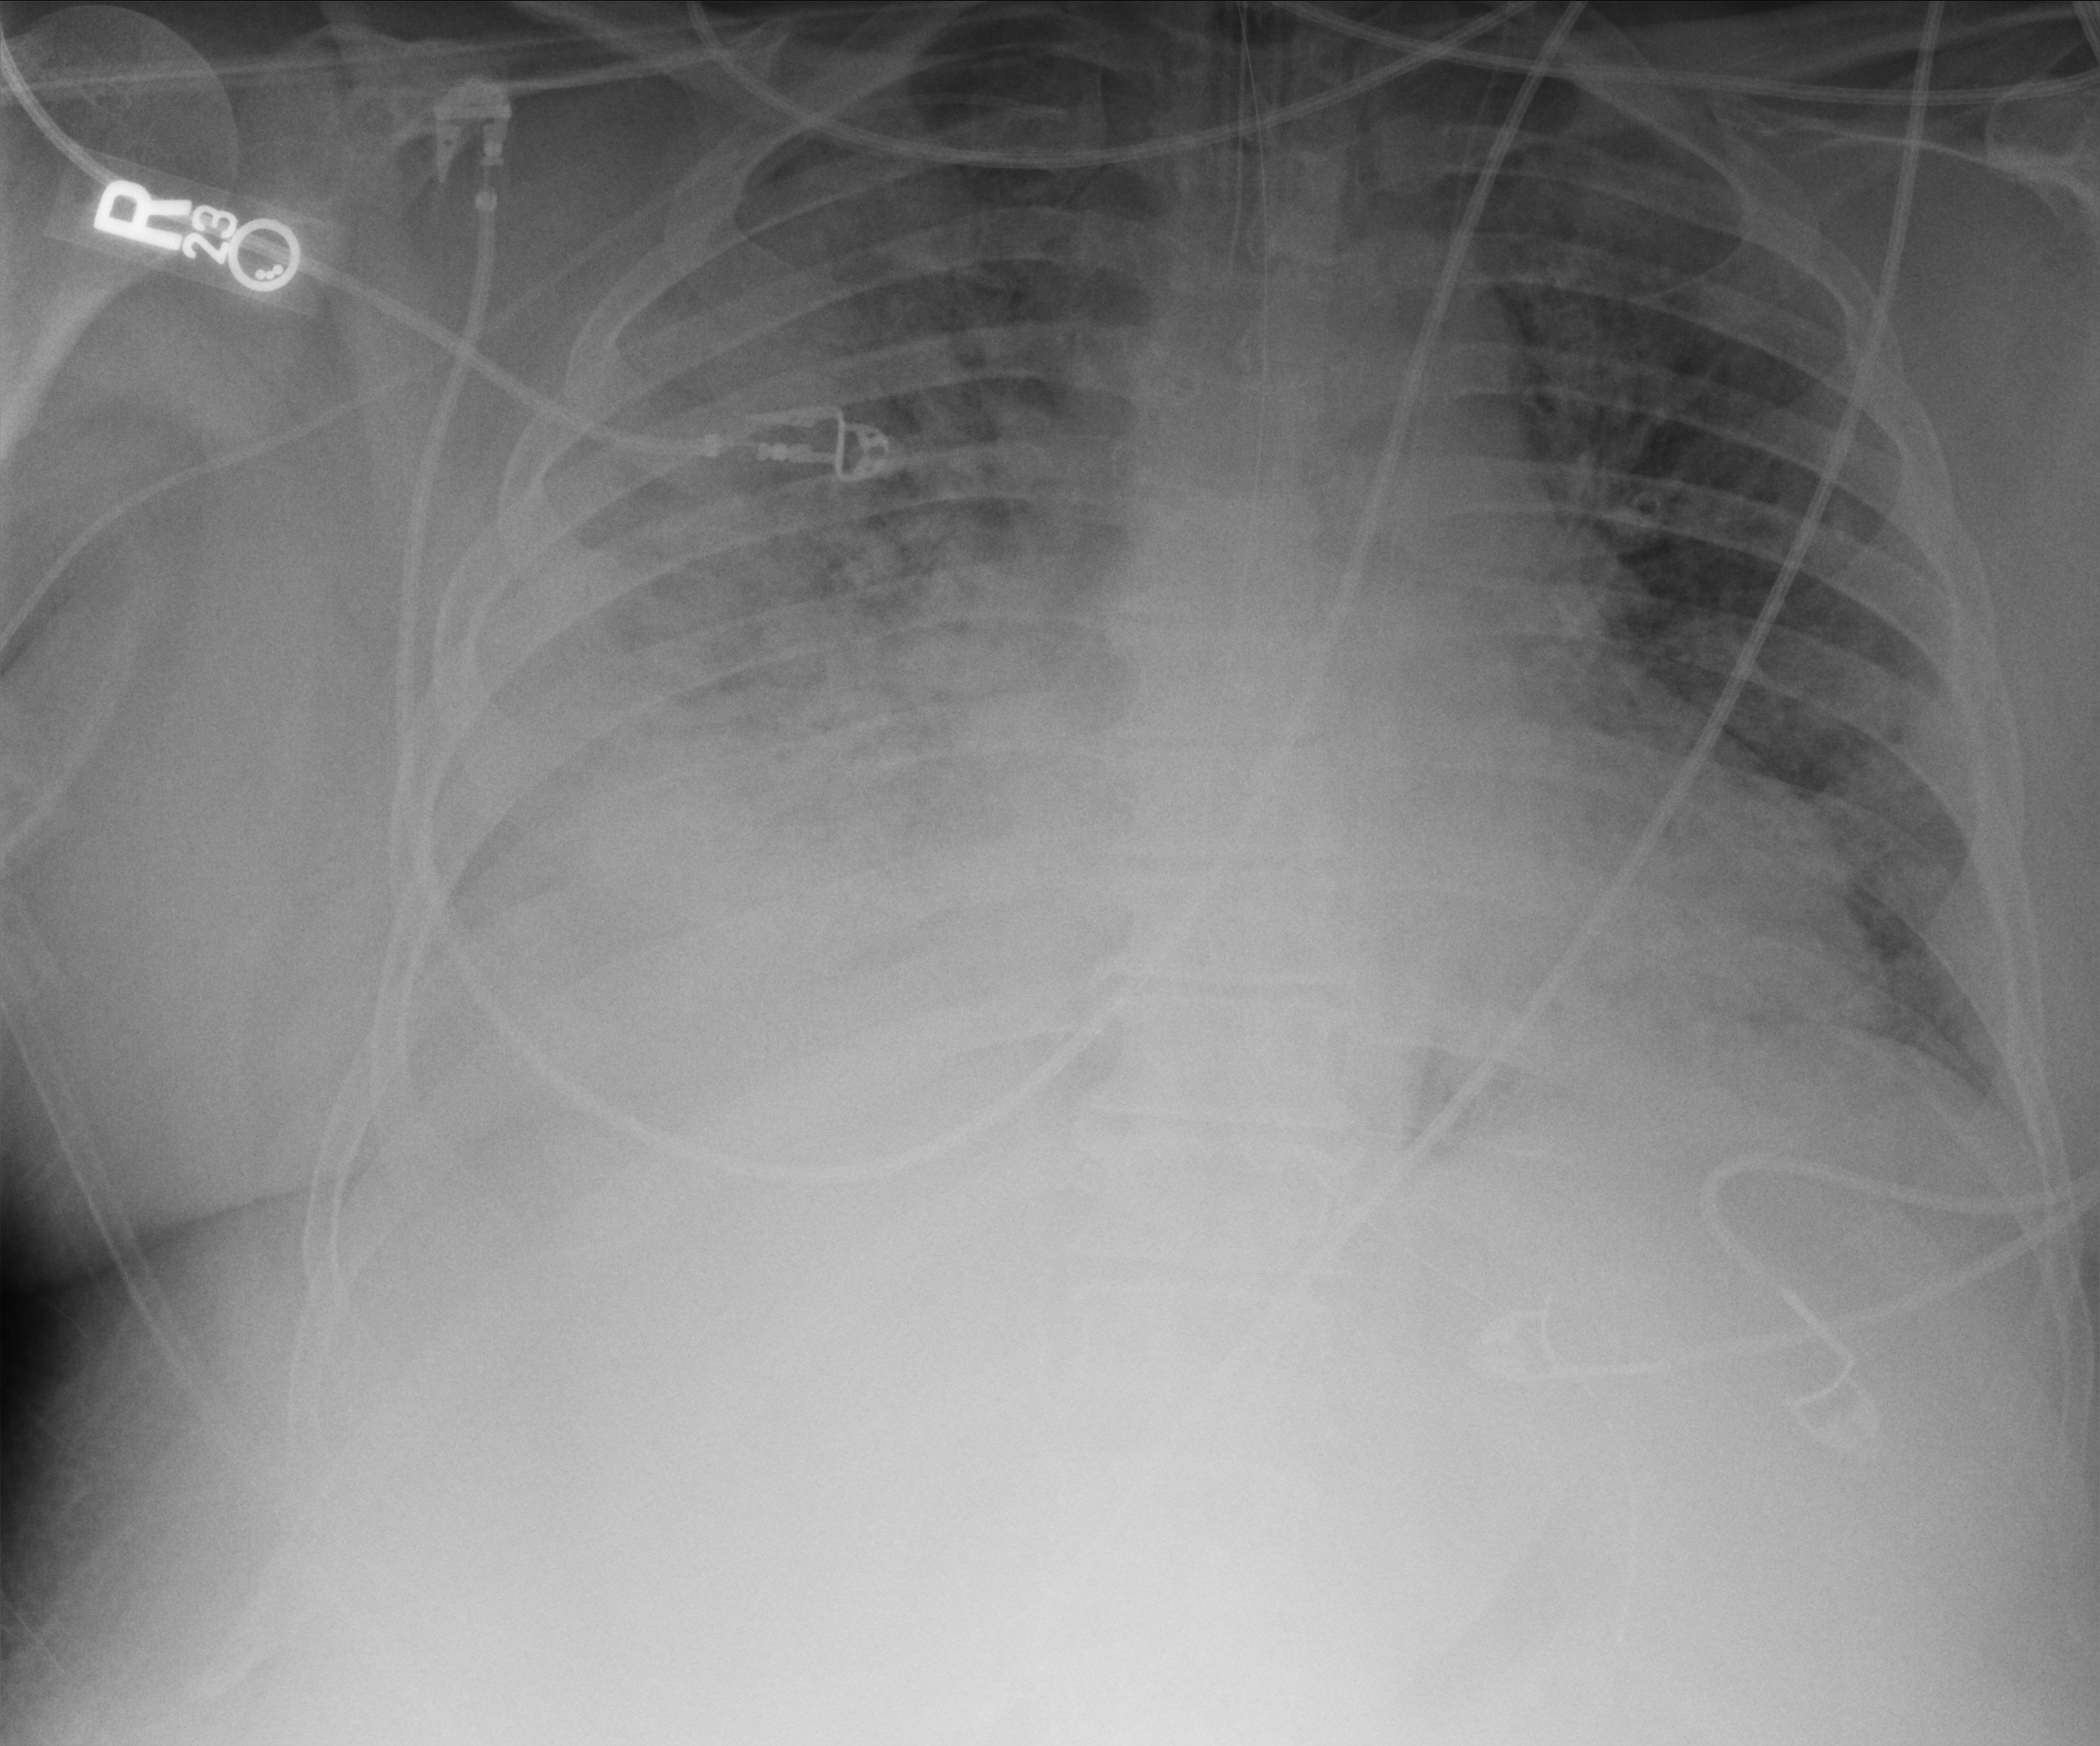
Chest X-ray (portable), anteroposterior (AP) projection. Patient hospitalised with COVID-19; male, aged 18–59 years.
From the hospital-stay record, not from the radiograph (when in the stay this image was taken is not recorded):
- other chronic lung disease (admission record): no
- admitted to intensive care during this hospital stay: yes
- mechanically ventilated during this hospital stay: yes